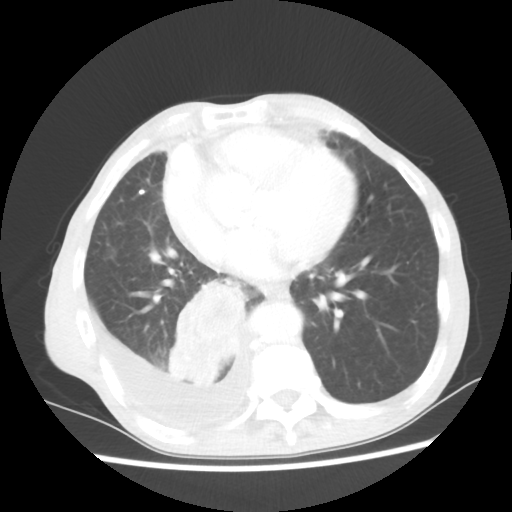
Chest CT, one axial slice. Slice 23 of 60 in the series (ordered by position). Lung window (W 1500 / L -600 HU). 512 × 512 image matrix. Patient: male, 76 years. Case-level facts recorded for this patient, not image findings: clinical TNM (as recorded): T3 N3 M1a; histopathological grade: G3.
Structures marked on this image (rectangle marked by the reading radiologist):
- lung tumour (recorded histology: squamous cell carcinoma): bounding box [x1, y1, x2, y2] px = [161, 274, 248, 393]